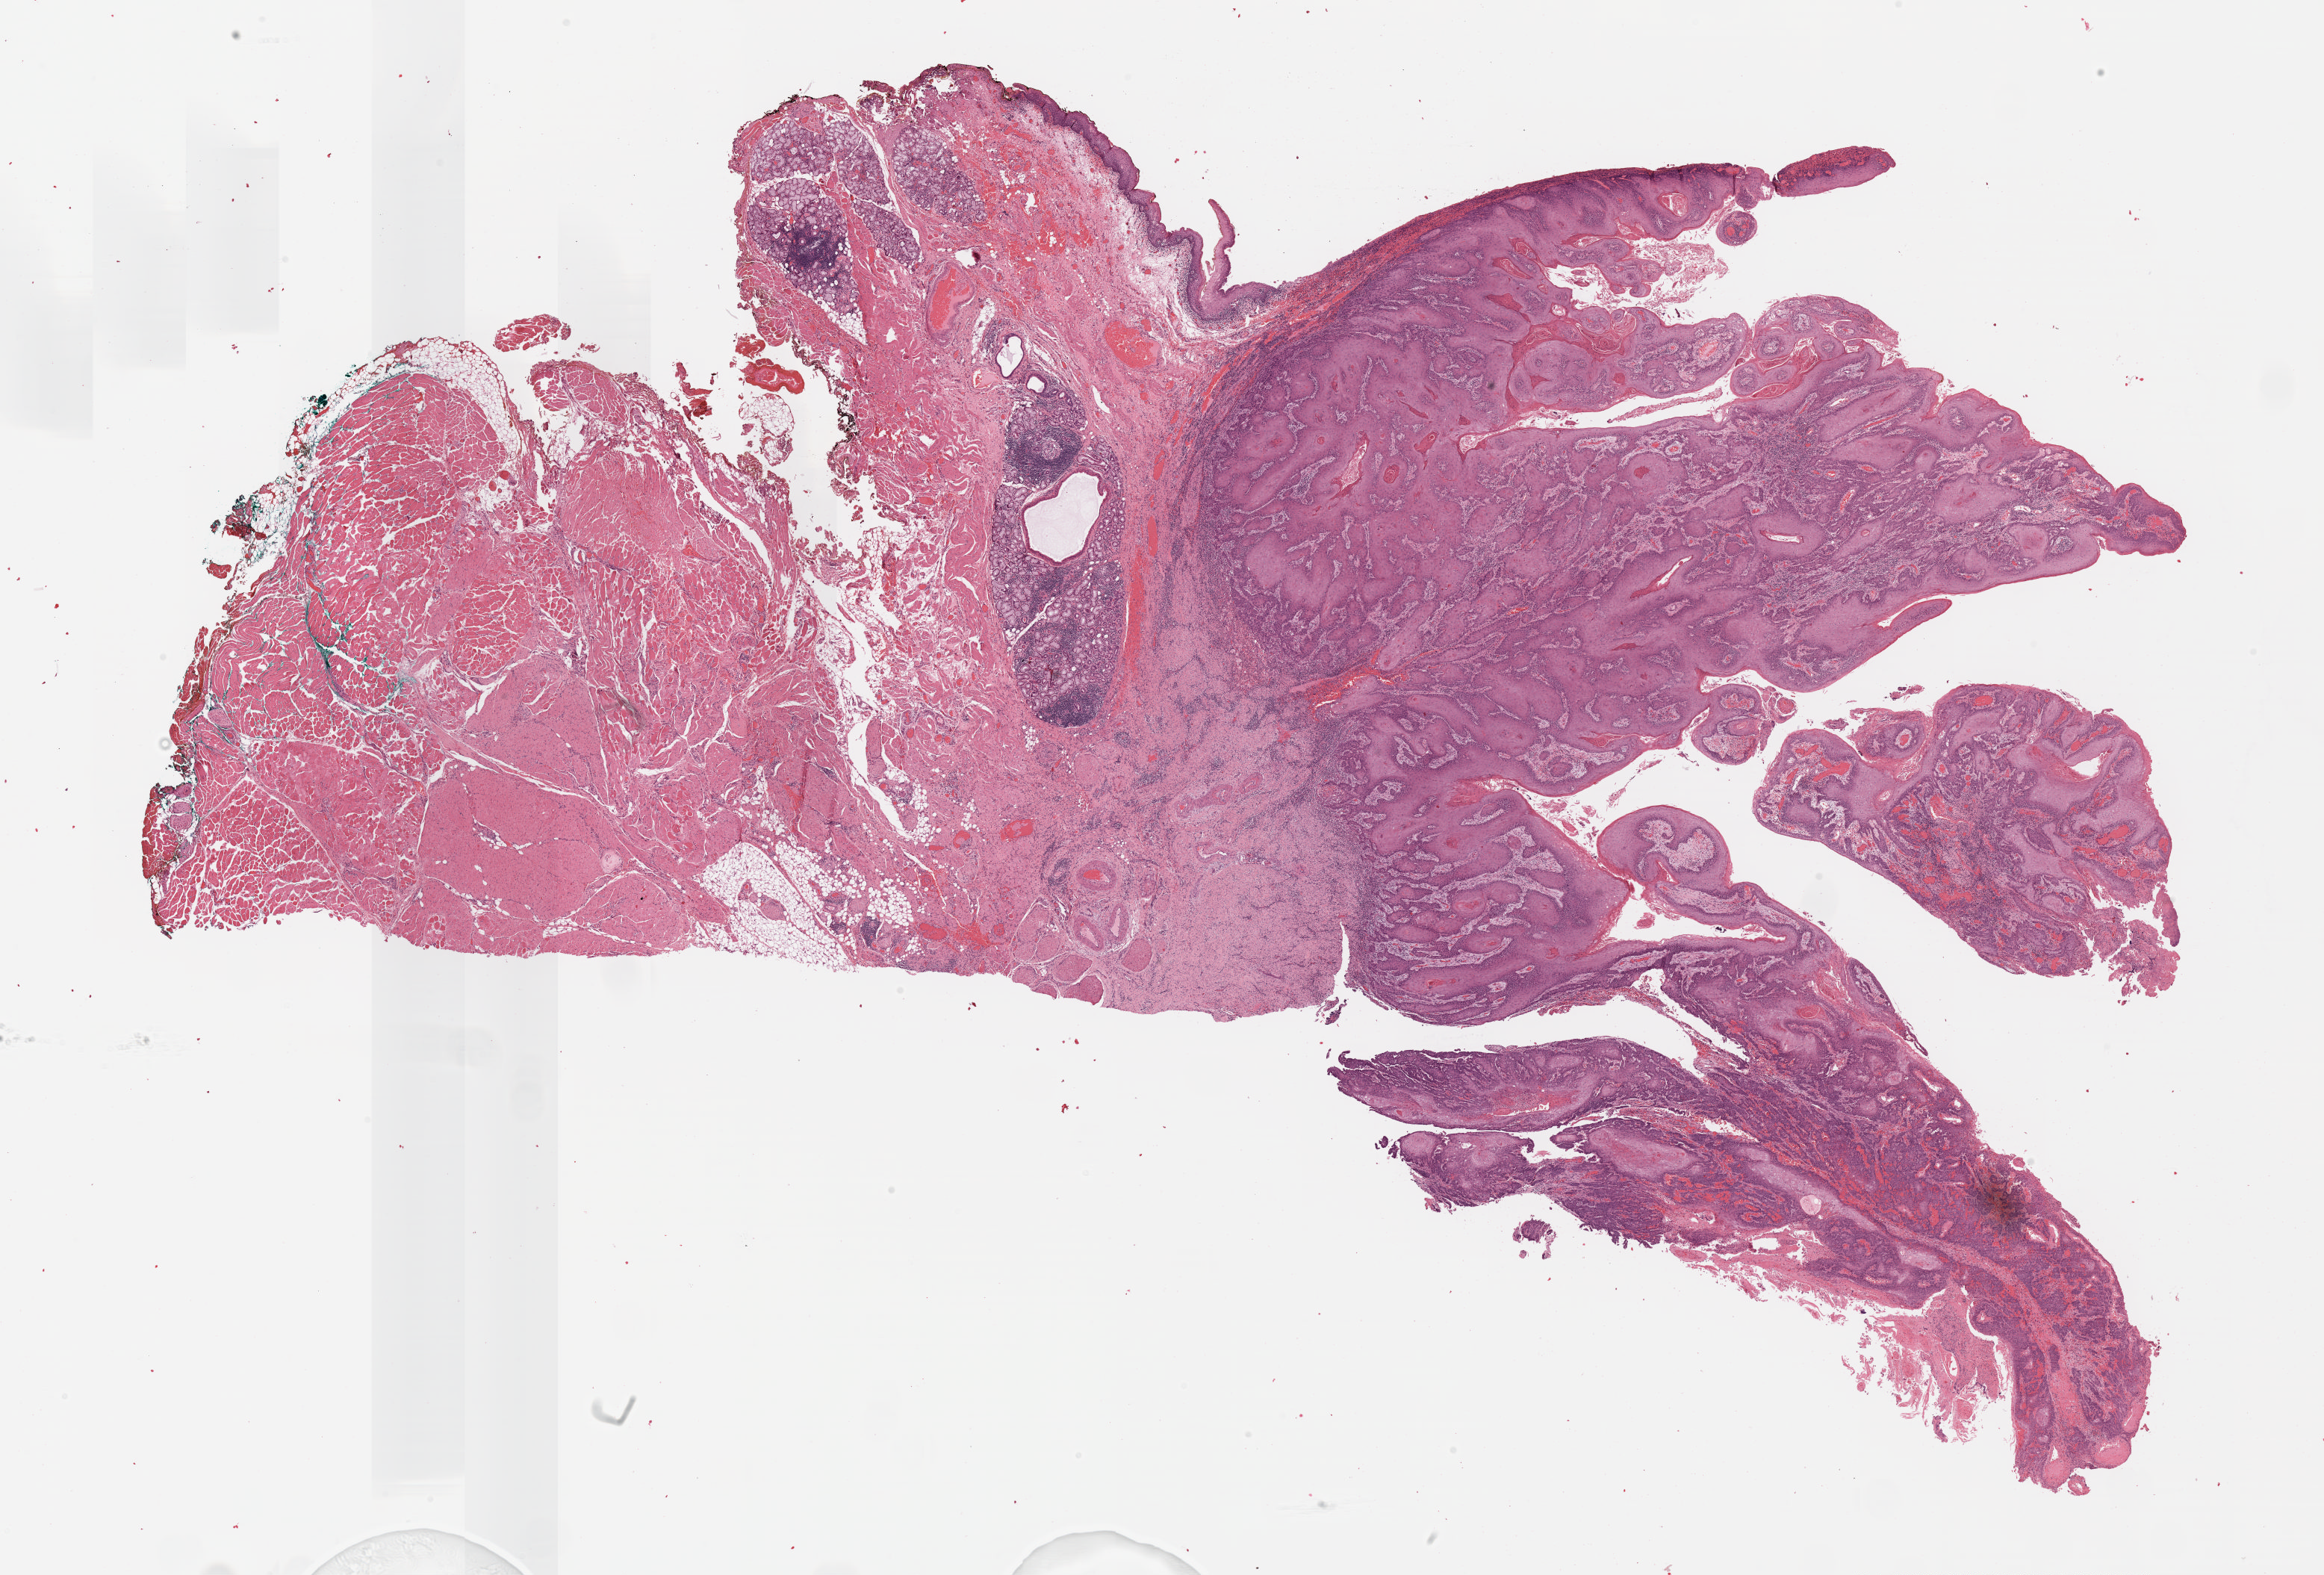
Whole-slide histology image, H&E, low-resolution overview of the scanned area, about 24.7 x 16.8 mm. FFPE section. Primary tumour sample from the head and neck. Female patient; age at initial diagnosis 76 years. Histologic grade: G2 (moderately differentiated).
- AJCC pathologic stage: III (7th edition)
- pathologic diagnosis: Squamous cell carcinoma, NOS
- TNM: T2 N1 M0
- laterality: left